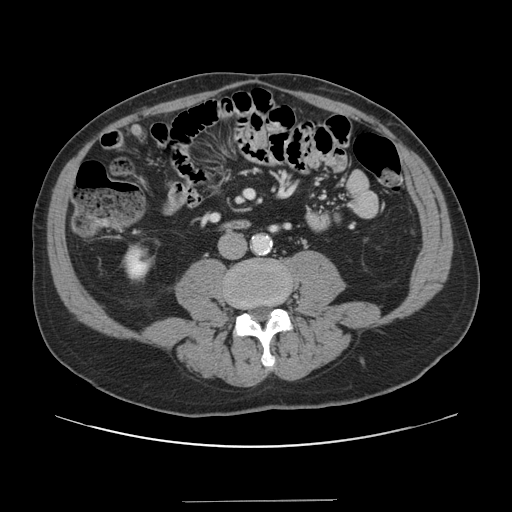
Contrast-enhanced abdominal CT, one axial slice. Slice 16 of 151 in the series (ordered by position). Intravenous contrast given. Soft-tissue window (W 400 / L 40 HU). 512 × 512 image matrix, field of view 399 × 399 mm. Male patient, age 63 years. Case-level facts recorded for this patient, not image findings: diagnosis: colorectal cancer liver metastases, imaged before liver resection; multiple liver metastases: no; largest metastasis: 2.1 cm.
Outlined on this slice (expert manual segmentation):
- portal vein (with intrahepatic branches): bounding box <247,193,253,197> (left, top, right, bottom; pixels)